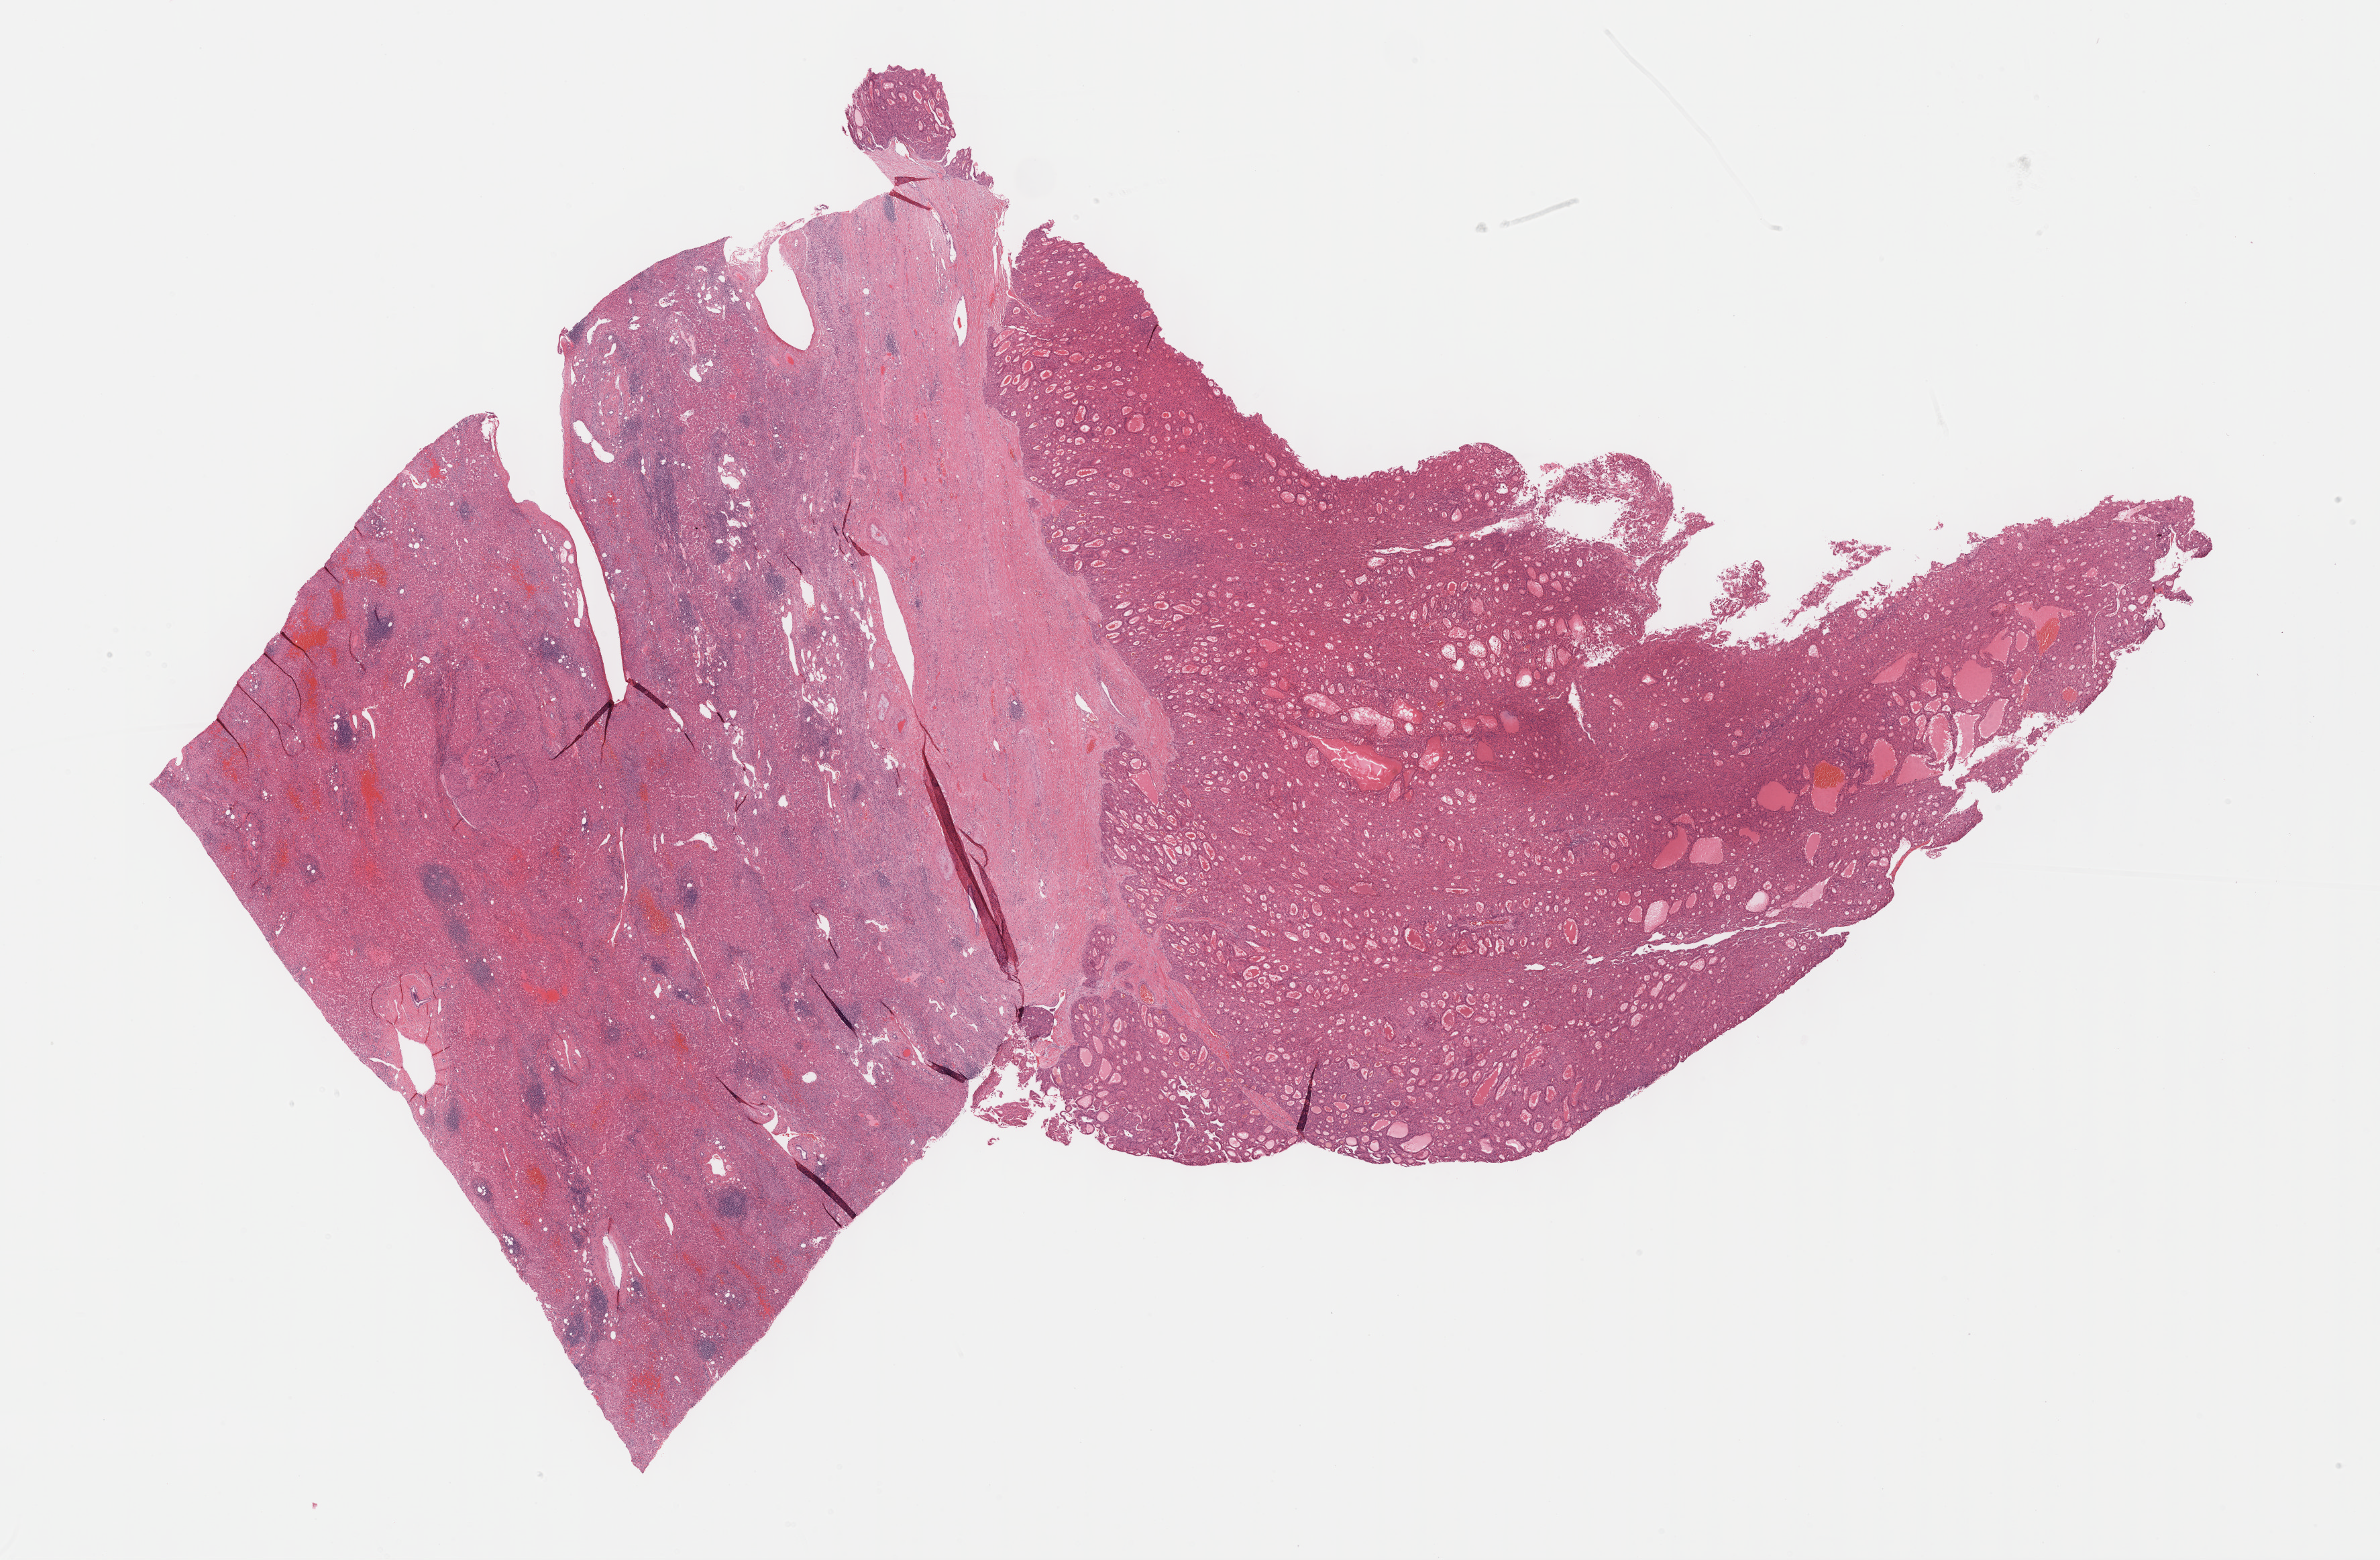
Digitized Hematoxylin and eosin (H&E) stained tissue section (whole slide) — a low-resolution overview of the entire scanned area, about 28.7 x 18.8 mm. Formalin-fixed paraffin-embedded (FFPE) diagnostic section. Sample: primary tumour, liver. Patient: male, age at initial diagnosis 52 years.
Pathologic diagnosis: Hepatocellular carcinoma, NOS.